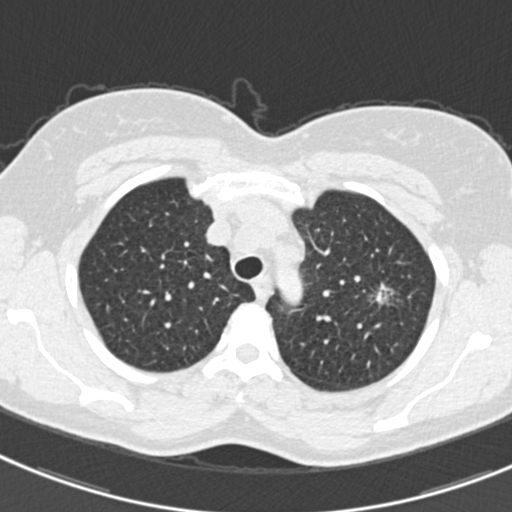
Low-dose screening chest CT, one axial slice; slice 250 of 309 in the series (ordered by position); lung window (W 1500 / L -600 HU); 1 mm slice thickness; 512 × 512 image matrix, field of view 302 × 302 mm.
Structures marked on this image (expert manual segmentation):
- lesion 1 (tumor, upper lobe of left lung): bounding box <378,294,387,302> (left, top, right, bottom; pixels)